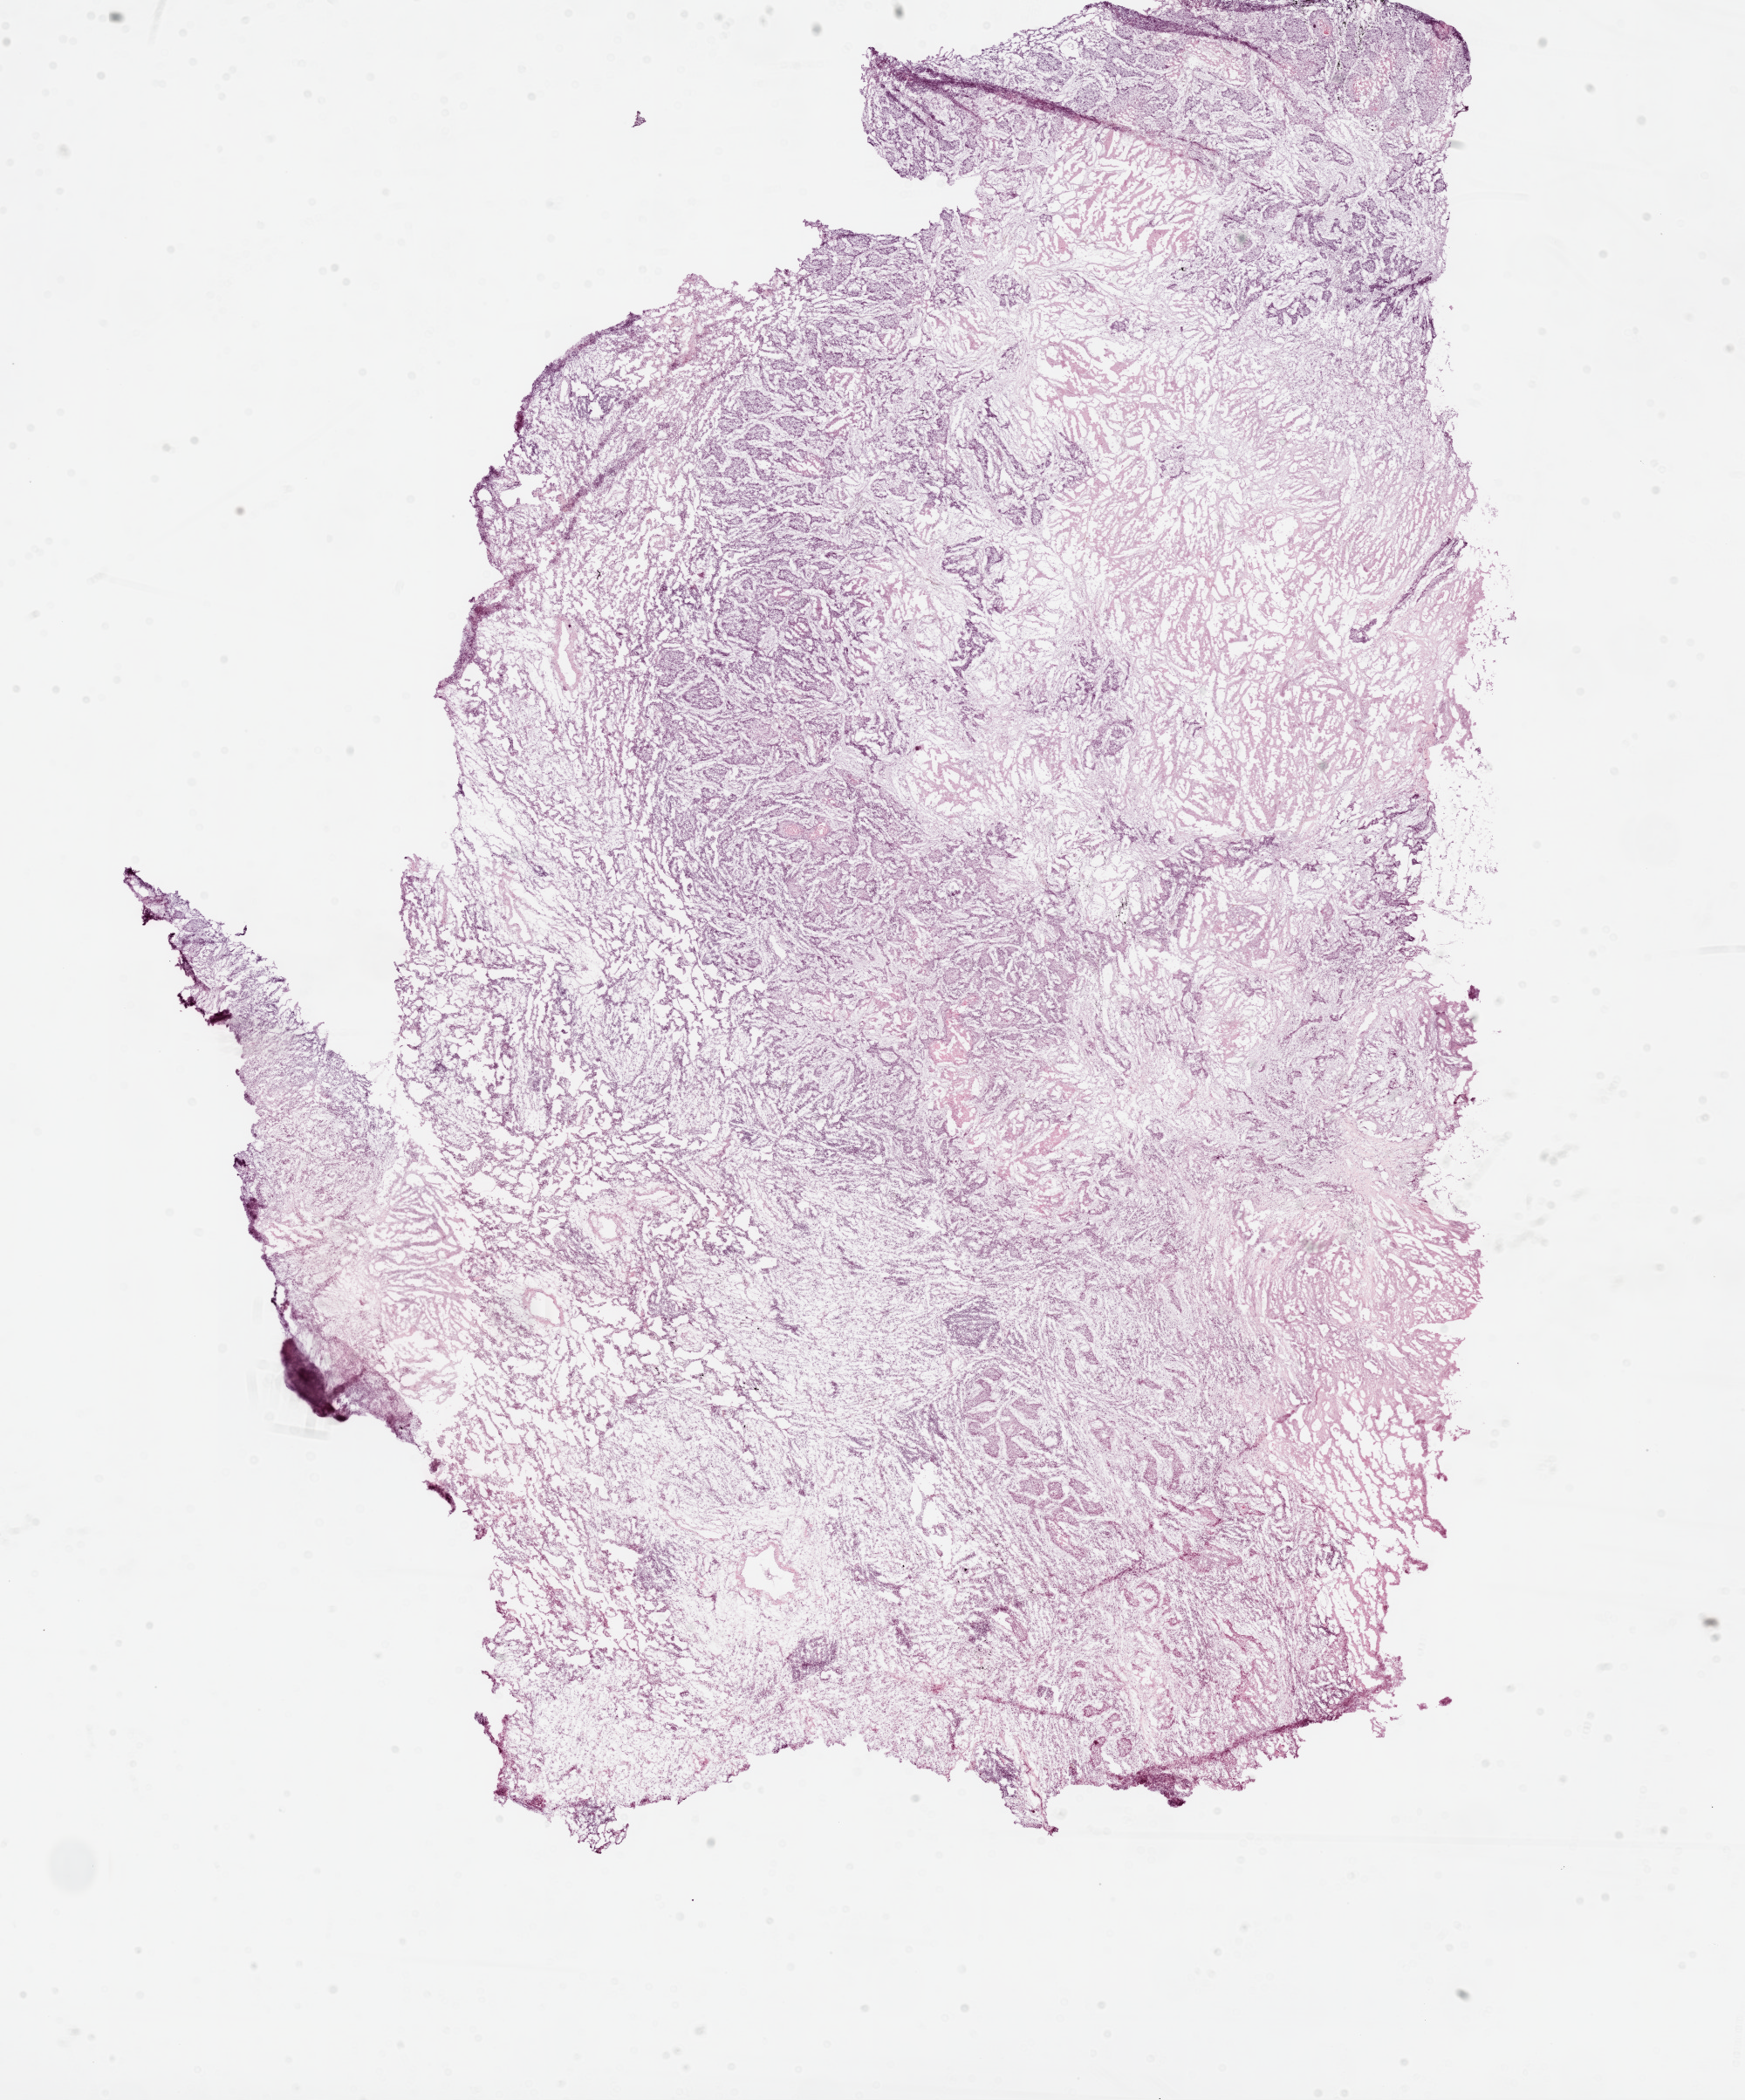
Whole-slide histology image, H&E-stained — whole scanned area (about 16.0 x 19.3 mm, acquisition: 20x scan) shown as a low-resolution overview; frozen section; sample: primary tumour, lung. Patient: male, age at initial diagnosis 73 years. Slide review estimates, as recorded: tumour cells 55%, tumour nuclei 70%, normal cells 0%, stromal cells 15%, necrosis 30%.
• TNM: T2 N1 M0
• diagnosis: Squamous cell carcinoma, NOS (upper lobe, lung)
• AJCC pathologic stage: IIB (6th edition)